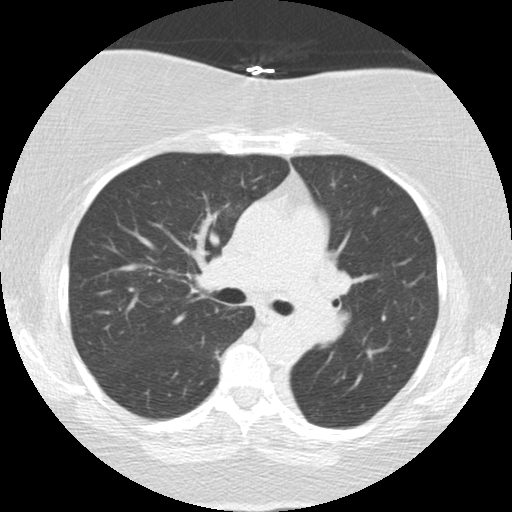
Low-dose screening chest CT, one axial slice. Slice 83 of 136 in the series (ordered by position). Lung window (W 1500 / L -600 HU). 2.5 mm slice thickness. 512 × 512 image matrix, field of view 309 × 309 mm.
Structures marked on this image (manually delineated by an expert):
- lesion 2 (tumor, mediastinum): box from (x=287, y=262) to (x=352, y=344) px